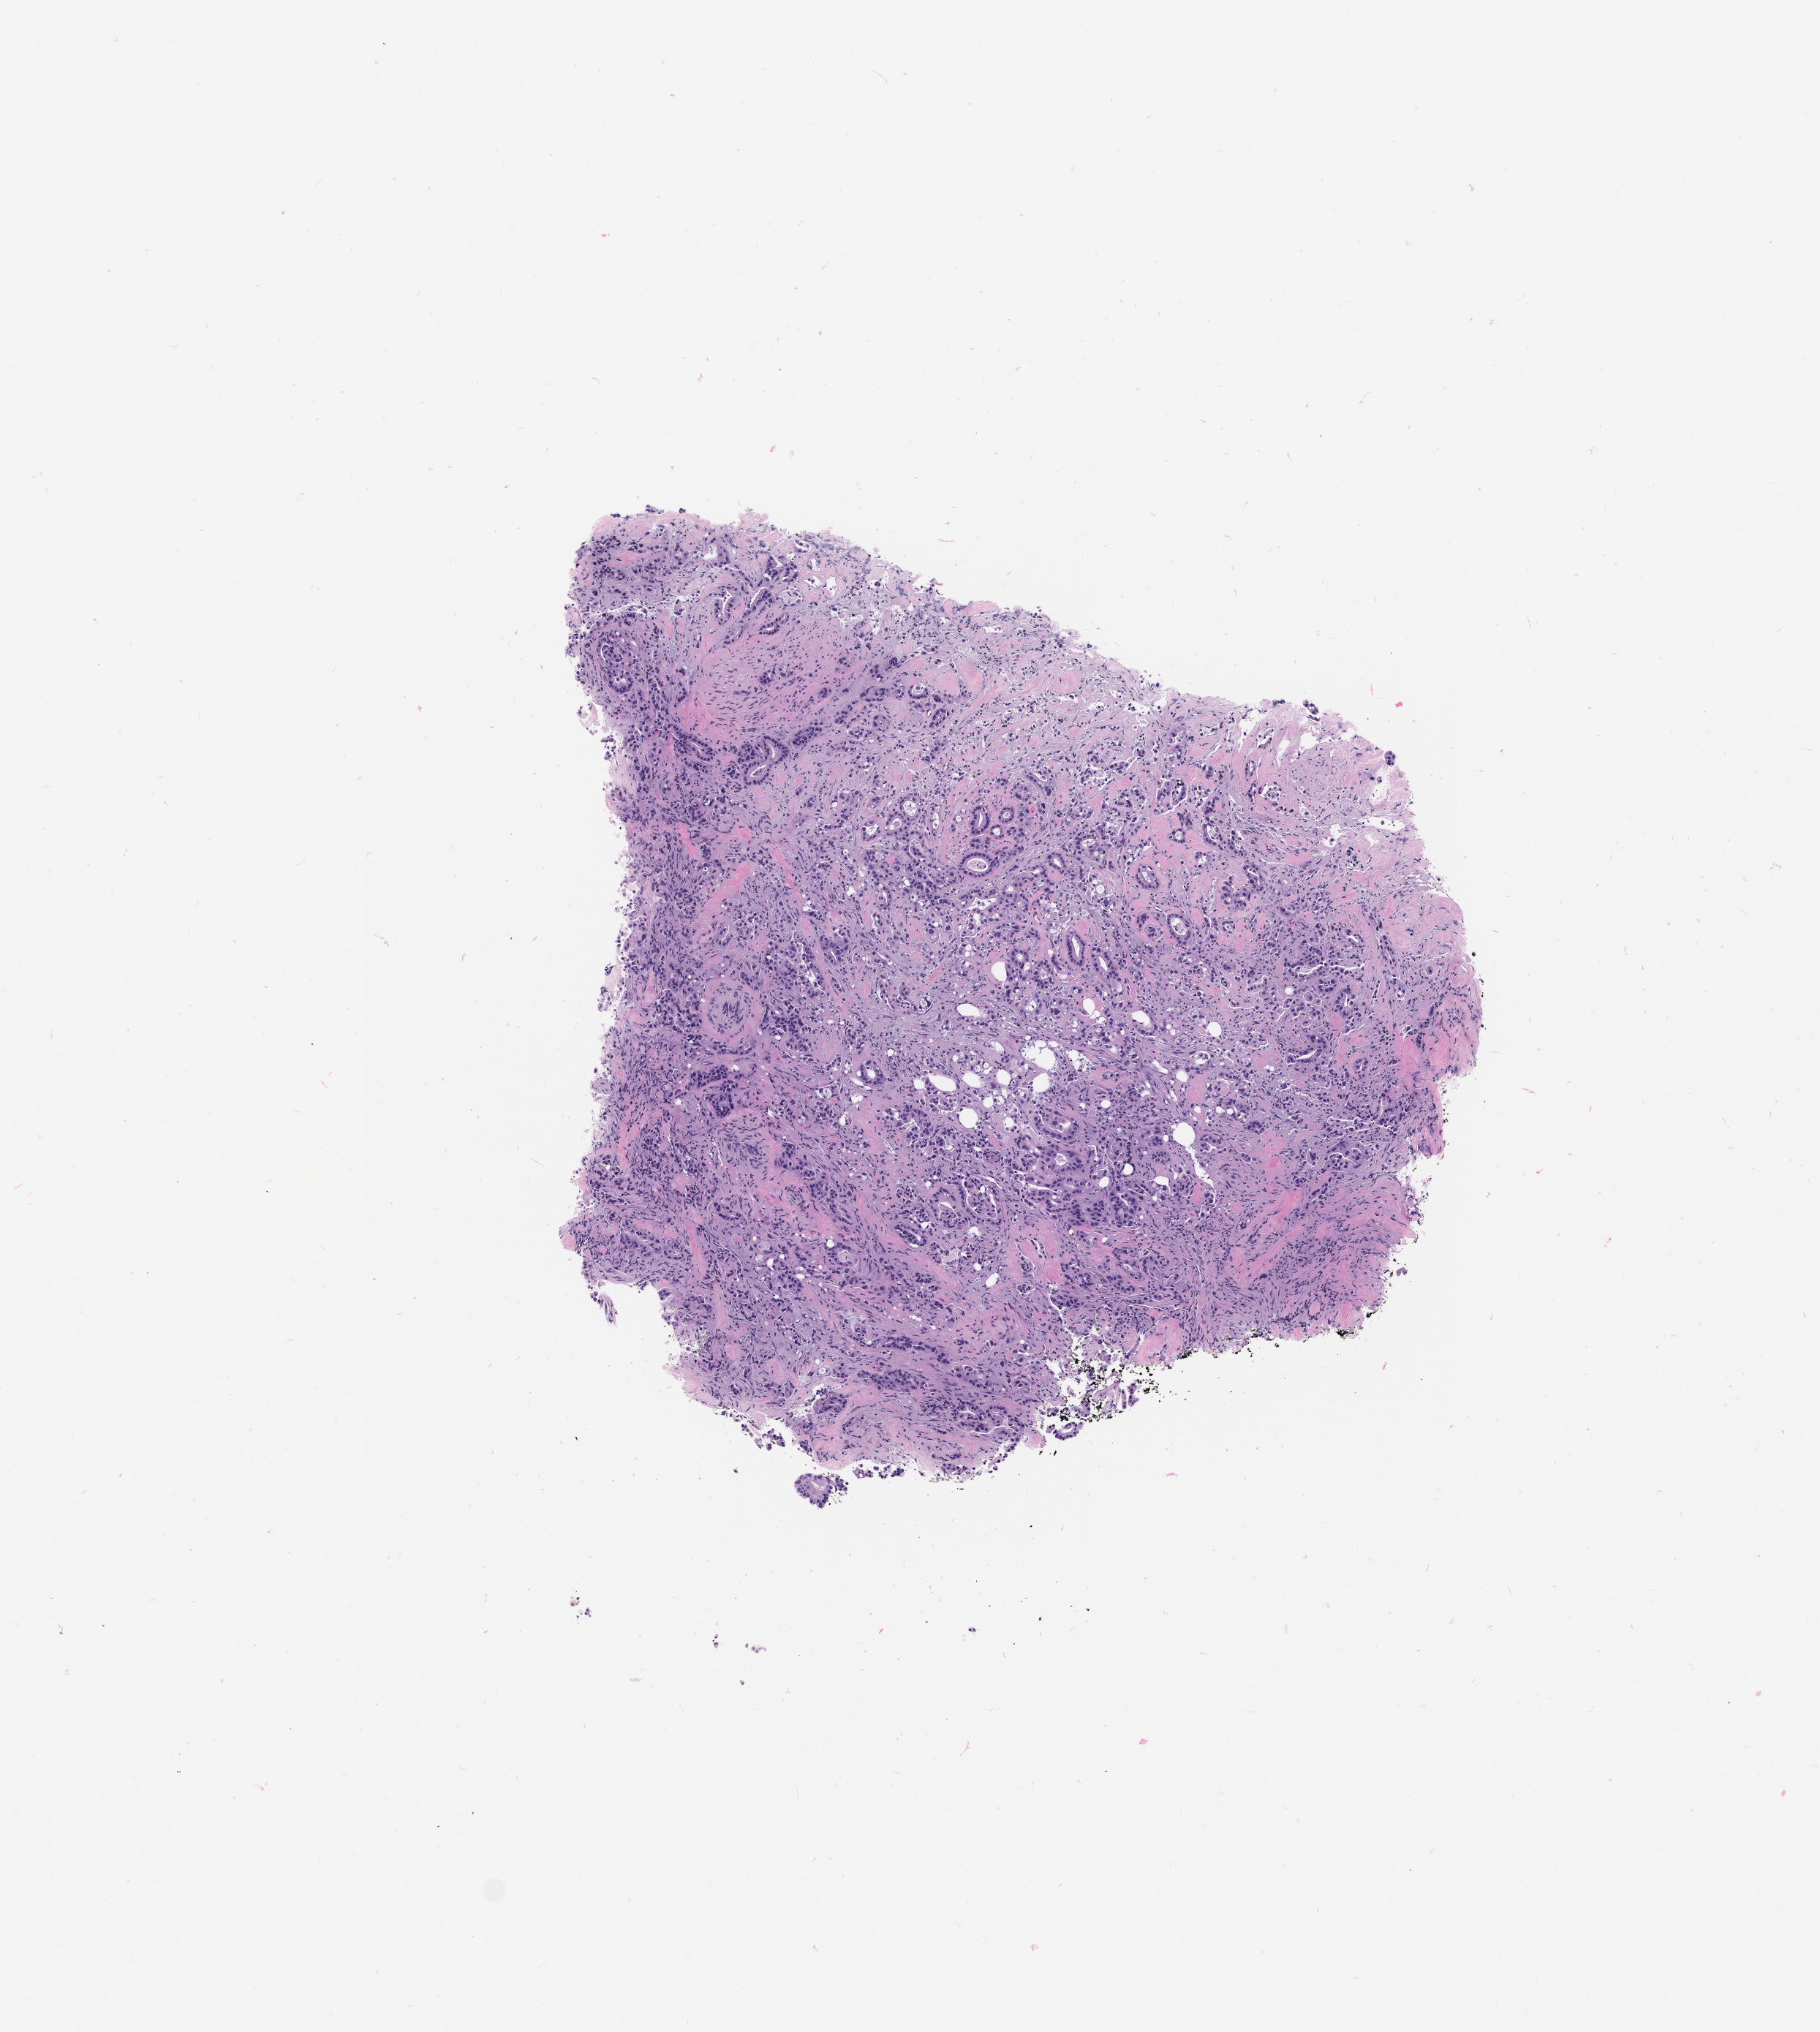
Hematoxylin and eosin (H&E) whole-slide image of the patient's (originator) tumor tissue, shown as a low-resolution overview of the whole scanned area (about 5.0 x 5.6 mm). Formalin-fixed paraffin-embedded section. Tumor site category: pancreas. Patient: male, 70 years old.
Diagnosis: Pancreatic Adenocarcinoma.